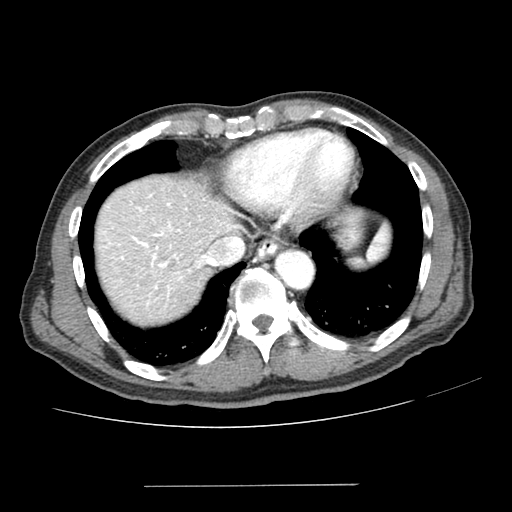
Contrast-enhanced abdominal CT (liver protocol), one axial slice; slice 175 of 187 in the series (ordered by position); one of 2 acquisitions stored at this slice position; soft-tissue window (W 400 / L 40 HU); 2.5 mm slice thickness; 512 × 512 image matrix, field of view 360 × 360 mm. From the clinical record (not read from this slice): diagnosis: hepatocellular carcinoma (patient treated with transarterial chemoembolisation; whether this scan precedes or follows treatment is not stated here); TNM stage (as recorded): Stage-I; Child-Pugh class: A.
Structures marked on this image (semi-automatic segmentation, software-assisted and operator-edited):
- abdominal aorta: bounding box (x1, y1, x2, y2) in pixels: (275, 249, 313, 287)
- liver parenchyma outside the tumour (the mass and vessels are separate outlines, so this box may not span the whole liver): (96, 176, 239, 322)
- mass: (124, 259, 148, 281)
- liver vessels: (103, 194, 230, 305)